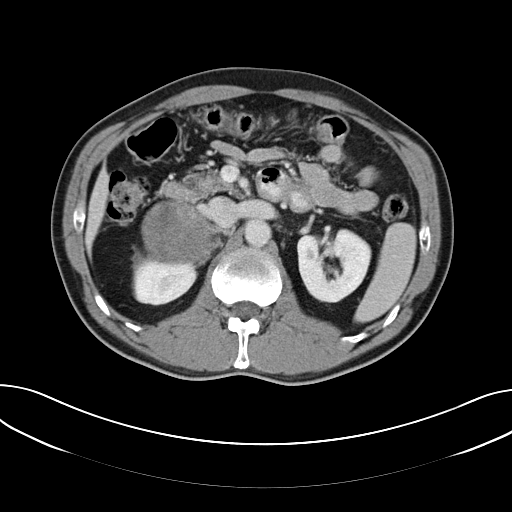
Contrast-enhanced abdominal CT, one axial slice. Position 30 of 61 along the scan axis. 120 kVp. Intravenous contrast given. Soft-tissue window (W 400 / L 40 HU). 5 mm slice thickness. 512 × 512 image matrix, field of view 372 × 372 mm. Patient: male, 57 years. Case-level facts recorded for this patient, not image findings: diagnosis: adrenocortical carcinoma; tumour side: right adrenal; tumour size at pathology: 11.2 cm; Ki-67 index: 10 %; stage (as recorded): 3.
Structures marked on this image (semi-automatically segmented with operator editing):
- mass: bounding box [x1, y1, x2, y2] px = [142, 202, 215, 263]